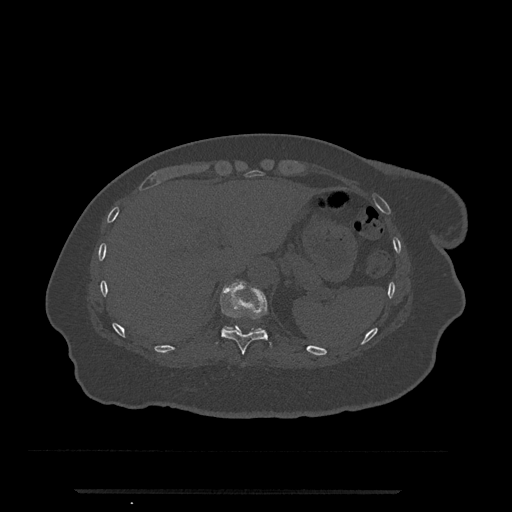
CT including the spine, one axial slice. Slice 273 of 797 in the series (ordered by position). Reconstruction kernel Br40s/3. Bone window (W 1800 / L 400 HU). 0.5 mm slice thickness. 512 × 512 image matrix. Female patient, age 51 years. Case-level facts recorded for this patient, not image findings: primary cancer: neuro; vertebrae with lytic lesions (as recorded): T8.
Annotated regions visible in this slice (semi-automatic segmentation, software-assisted and operator-edited):
- T10 vertebra: bounding box (x1, y1, x2, y2) in pixels: (215, 279, 272, 364)
- T11 vertebra: (226, 326, 260, 330)